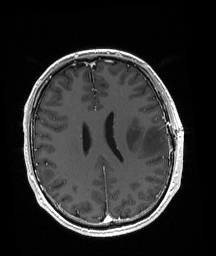
Brain MRI from a brain-tumour surgery series, one axial slice; slice 76 of 192 in the series (ordered by position); T1-weighted post-contrast; 1 mm slice thickness; 216 × 256 image matrix, field of view 211 × 250 mm. Case-level facts recorded for this patient, not image findings: histopathology: Astrocytoma; WHO grade: 3; IDH mutation: yes.
Outlined on this slice (manually delineated by an expert):
- tumour: bounding box (x1, y1, x2, y2) in pixels: (126, 126, 166, 155)